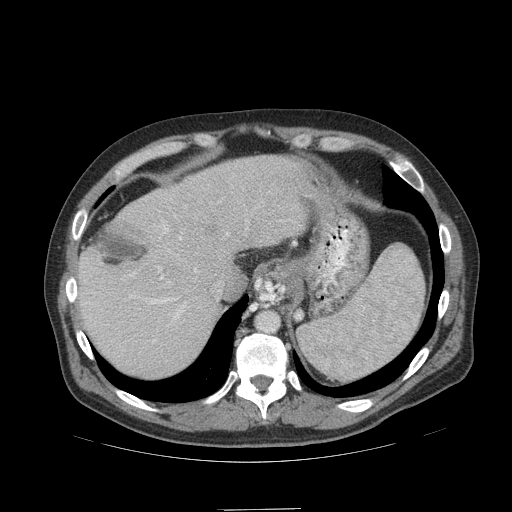
Contrast-enhanced abdominal CT (liver protocol), one axial slice; slice 80 of 99 in the series (ordered by position); reconstruction kernel STANDARD; 140 kVp; soft-tissue window (W 400 / L 40 HU); 2.5 mm slice thickness; 512 × 512 image matrix, field of view 440 × 440 mm. From the clinical record (not read from this slice): diagnosis: hepatocellular carcinoma (patient treated with transarterial chemoembolisation; whether this scan precedes or follows treatment is not stated here); TNM stage (as recorded): Stage-I; Child-Pugh class: A; tumour differentiation: no biopsy; tumour nodularity: uninodular.
Structures marked on this image (semi-automatic segmentation, software-assisted and operator-edited):
- liver parenchyma outside the tumour (the mass and vessels are separate outlines, so this box may not span the whole liver): bounding box [x1, y1, x2, y2] px = [76, 154, 312, 377]
- mass: [203, 221, 221, 245]
- liver vessels: [85, 215, 248, 342]